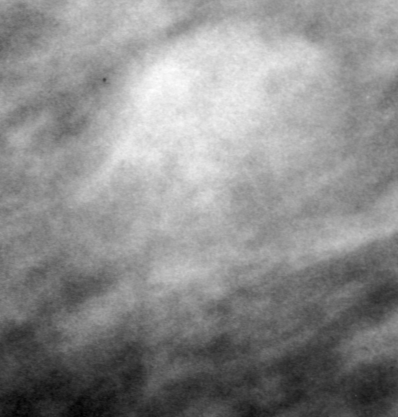
Cropped region of a digitized screen-film mammogram centred on a radiologist-marked abnormality; right breast; MLO view; BI-RADS breast density category 2 (scale 1–4).
Finding: mass, shape oval, margins microlobulated; BI-RADS assessment category 0 (incomplete: needs additional imaging); pathology result (as recorded, not read from the image): benign.